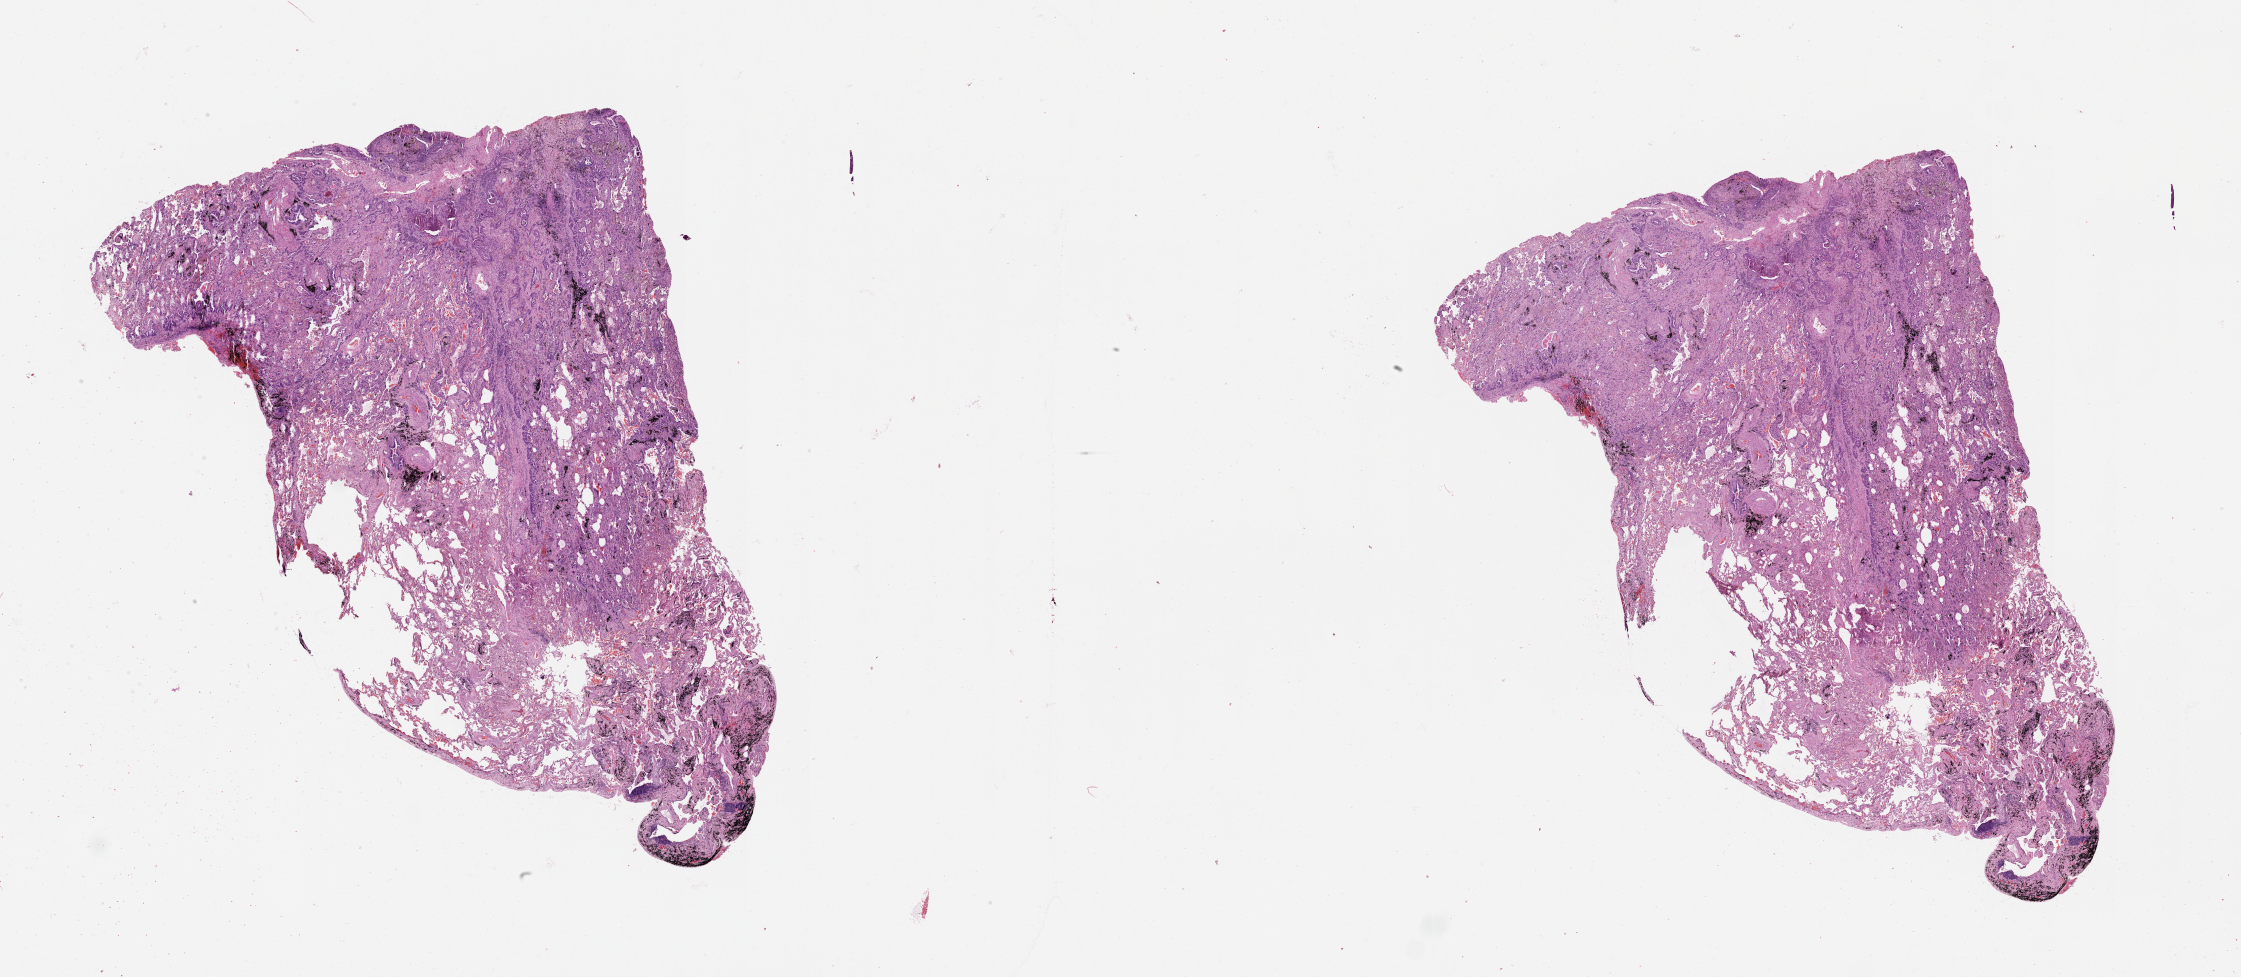
Whole-slide histology image, H&E-stained, shown as a low-resolution overview of the whole scanned area (about 36.1 x 15.7 mm, from a 20x scan), lung, tissue type not recorded.
Patient diagnosis (cohort enrolment): squamous cell carcinoma (lung).